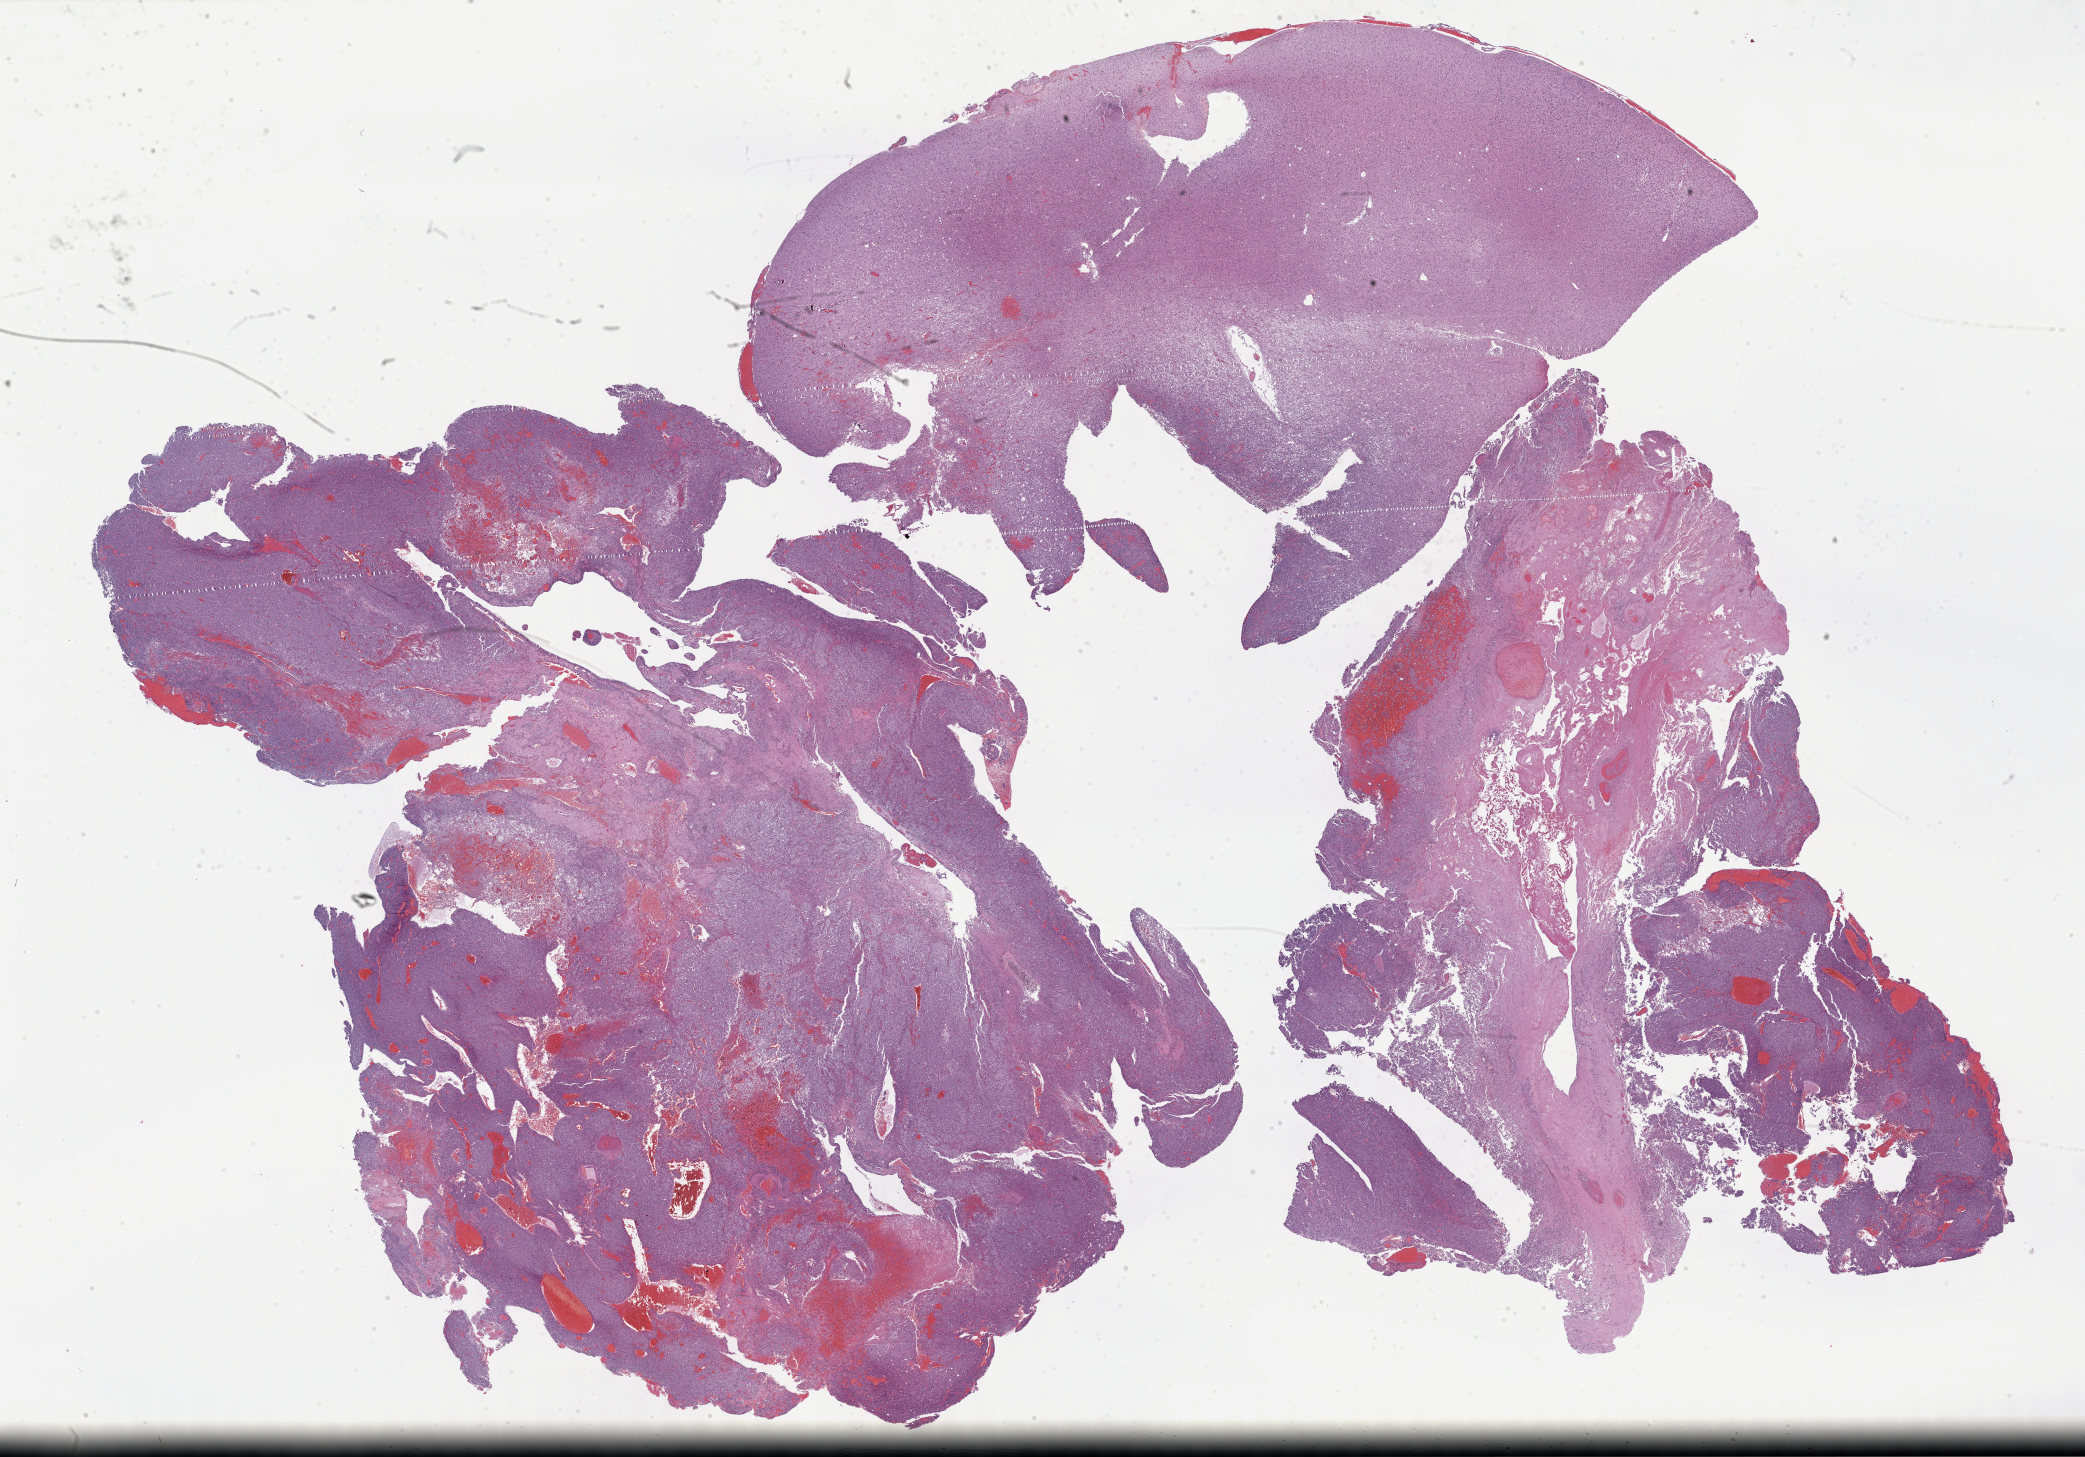
Whole-slide histology image, H&E-stained — whole scanned area (about 33.7 x 23.6 mm, from a 40x scan) shown as a low-resolution overview, formalin-fixed paraffin-embedded (FFPE) diagnostic section, sample: primary tumour, brain. Male patient; age at initial diagnosis 33 years. Histologic grade: G3 (poorly differentiated).
Pathologic diagnosis: Oligodendroglioma, anaplastic (cerebrum).